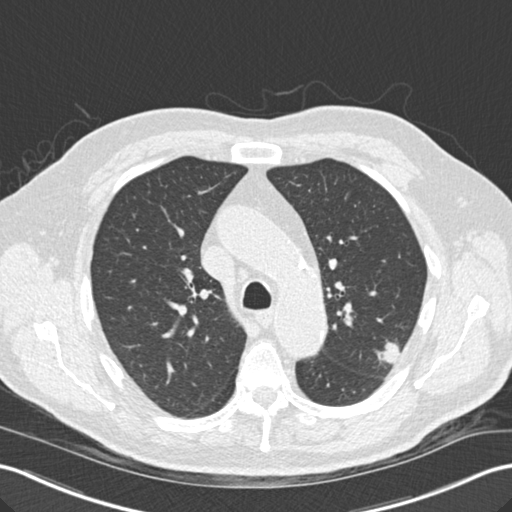
Low-dose screening chest CT, one axial slice. Position 106 of 157 along the scan axis. Reconstruction kernel B30f. 120 kVp. Lung window (W 1500 / L -600 HU). 2 mm slice thickness. 512 × 512 image matrix, field of view 354 × 354 mm.
Outlined on this slice (manually delineated by an expert):
- lesion 1 (tumor, upper lobe of left lung): bounding box <378,342,400,364> (left, top, right, bottom; pixels)